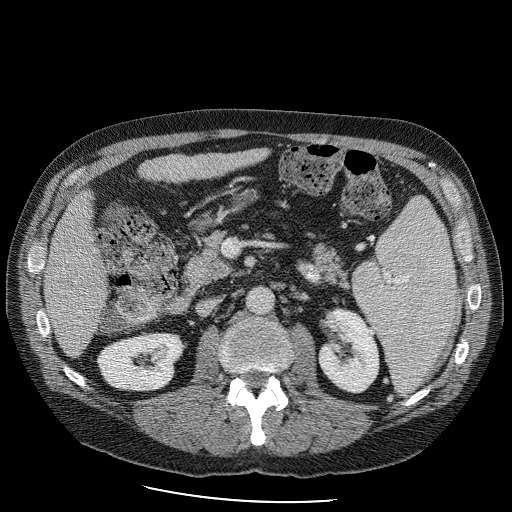
Contrast-enhanced abdominal CT (liver protocol), one axial slice. Position 34 of 98 along the scan axis. Reconstruction kernel STANDARD. 120 kVp. Soft-tissue window (W 400 / L 40 HU). 2.5 mm slice thickness. 512 × 512 image matrix, field of view 400 × 400 mm. Case-level facts recorded for this patient, not image findings: diagnosis: hepatocellular carcinoma (patient treated with transarterial chemoembolisation; whether this scan precedes or follows treatment is not stated here); TNM stage (as recorded): Stage-II; Child-Pugh class: B; tumour differentiation: moderately differentiated; tumour nodularity: uninodular.
Annotated regions visible in this slice (semi-automatically segmented with operator editing):
- liver parenchyma outside the tumour (the mass and vessels are separate outlines, so this box may not span the whole liver): bounding box <42,140,278,352> (left, top, right, bottom; pixels)
- liver vessels: <83,301,85,303>